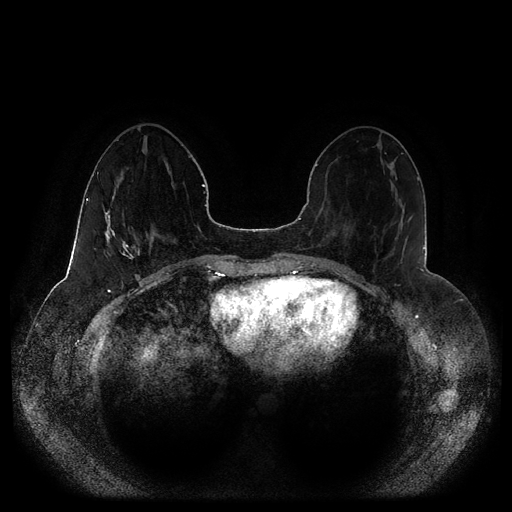
Breast MRI (dynamic contrast-enhanced, multi-phase), one axial slice. Slice 37 of 116 in the series (ordered by position). Dynamic contrast-enhanced series, time point 2 of 5 at this slice position (early post-contrast). 1.5 T. TE 2.5 ms, TR 5.2 ms. 2 mm slice thickness. 512 × 512 image matrix. Patient: female, 44 years.
Structures marked on this image (semi-automatically segmented with operator editing):
- breast lesion (labelled 'tumour' in the annotation; benign lesions carry a separate 'benign' label): bounding box [x1, y1, x2, y2] px = [97, 171, 140, 264]